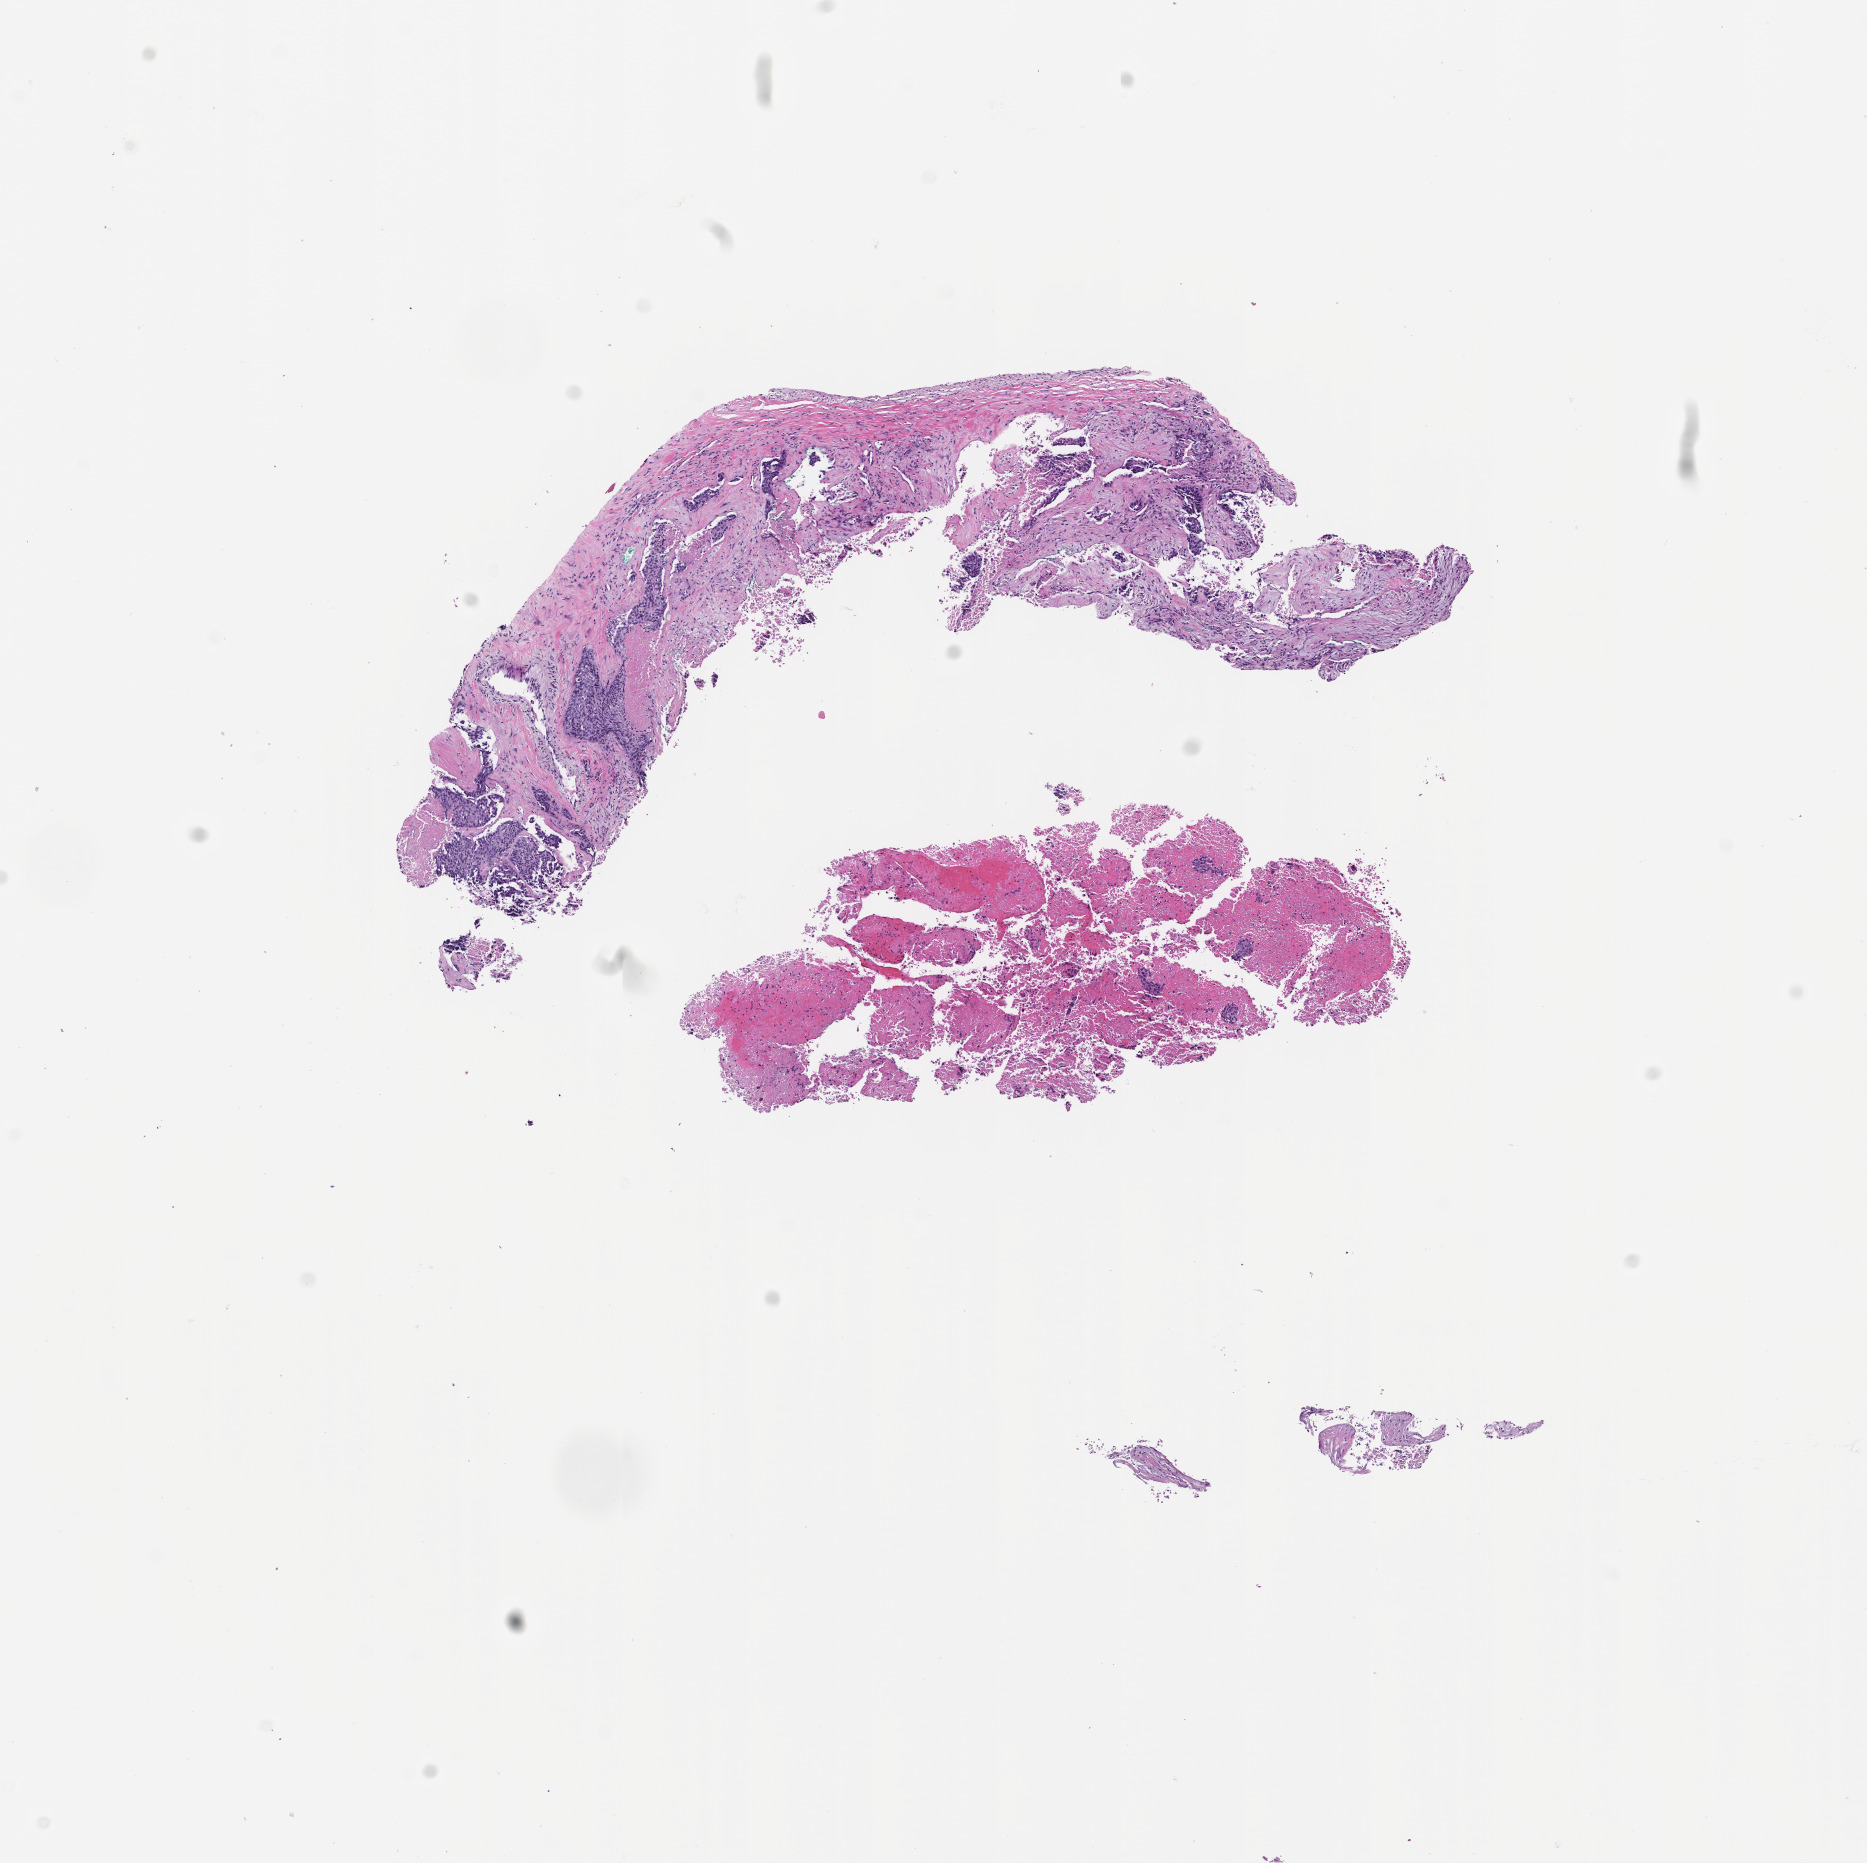
Whole-slide image, H&E stain, a low-resolution overview of the entire scanned area, about 7.5 x 7.5 mm; formalin-fixed, paraffin-embedded (FFPE) tissue; site: lung; specimen time point: archival tissue. Patient sex: female.
This section: primary tumor. Diagnosis: Non-Small Cell Lung Carcinoma.